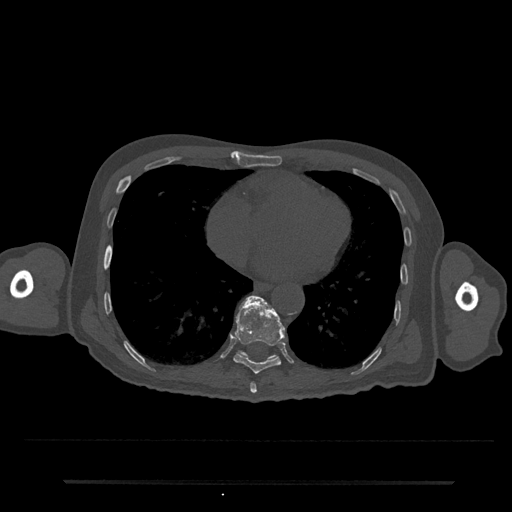
CT including the spine, one axial slice. Position 357 of 797 along the scan axis. 120 kVp. Bone window (W 1800 / L 400 HU). 0.5 mm slice thickness. 512 × 512 image matrix, field of view 427 × 427 mm. Patient: male, 74 years. From the clinical record (not read from this slice): primary cancer: prostate.
Annotated regions visible in this slice (semi-automatic segmentation, software-assisted and operator-edited):
- T10 vertebra: box from (x=238, y=303) to (x=276, y=360) px
- T8 vertebra: (x=250, y=382)–(x=257, y=394)
- T9 vertebra: (x=233, y=296)–(x=285, y=374)